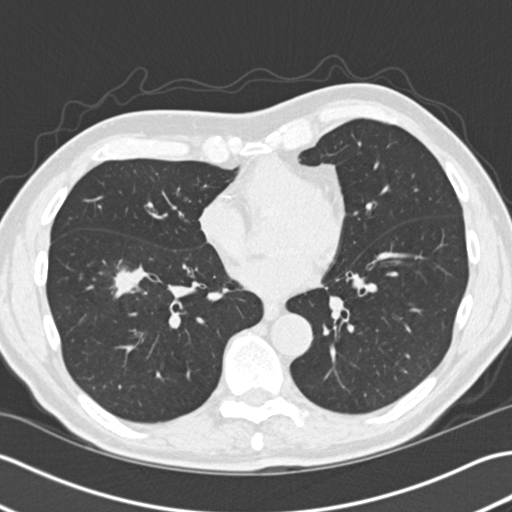
Axial slice from a low-dose chest CT screening exam, second annual screen, lung window (W 1500 / L -600 HU), 2 mm slice thickness, slice 104 of 172 in the series. Male, age 73 years at enrolment.
Expert reader's lesion annotation, box from (x=93, y=251) to (x=151, y=314) px. Reader record for this screening exam (exam-level; its link to the box is not recorded): non-calcified nodule or mass ≥4 mm, right lower lobe, 18 × 15 mm, spiculated (stellate) margins, soft tissue attenuation, pre-existing on the prior screen: yes. Participant outcome: lung cancer diagnosed 87 days after this screen — non-small cell carcinoma, right lower lobe, stage IA (AJCC 6th edition), 30 mm at pathology.